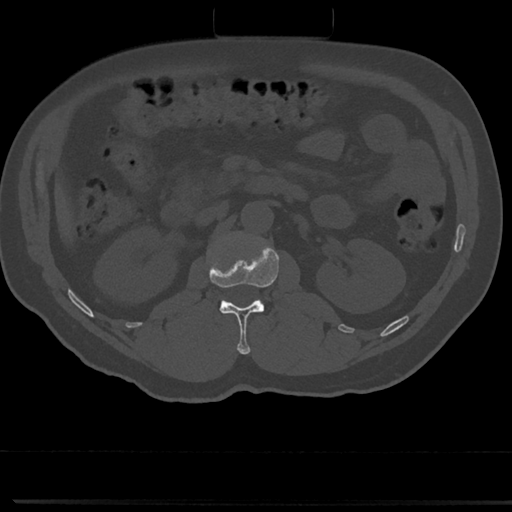
CT including the spine, one axial slice. Slice 65 of 817 in the series (ordered by position). 120 kVp. Bone window (W 1800 / L 400 HU). 512 × 512 image matrix, field of view 355 × 355 mm. Patient: male, 61 years. Case-level facts recorded for this patient, not image findings: primary cancer: prostate.
Annotated regions visible in this slice (semi-automatically segmented with operator editing):
- L1 vertebra: bounding box (x1, y1, x2, y2) in pixels: (205, 235, 300, 354)